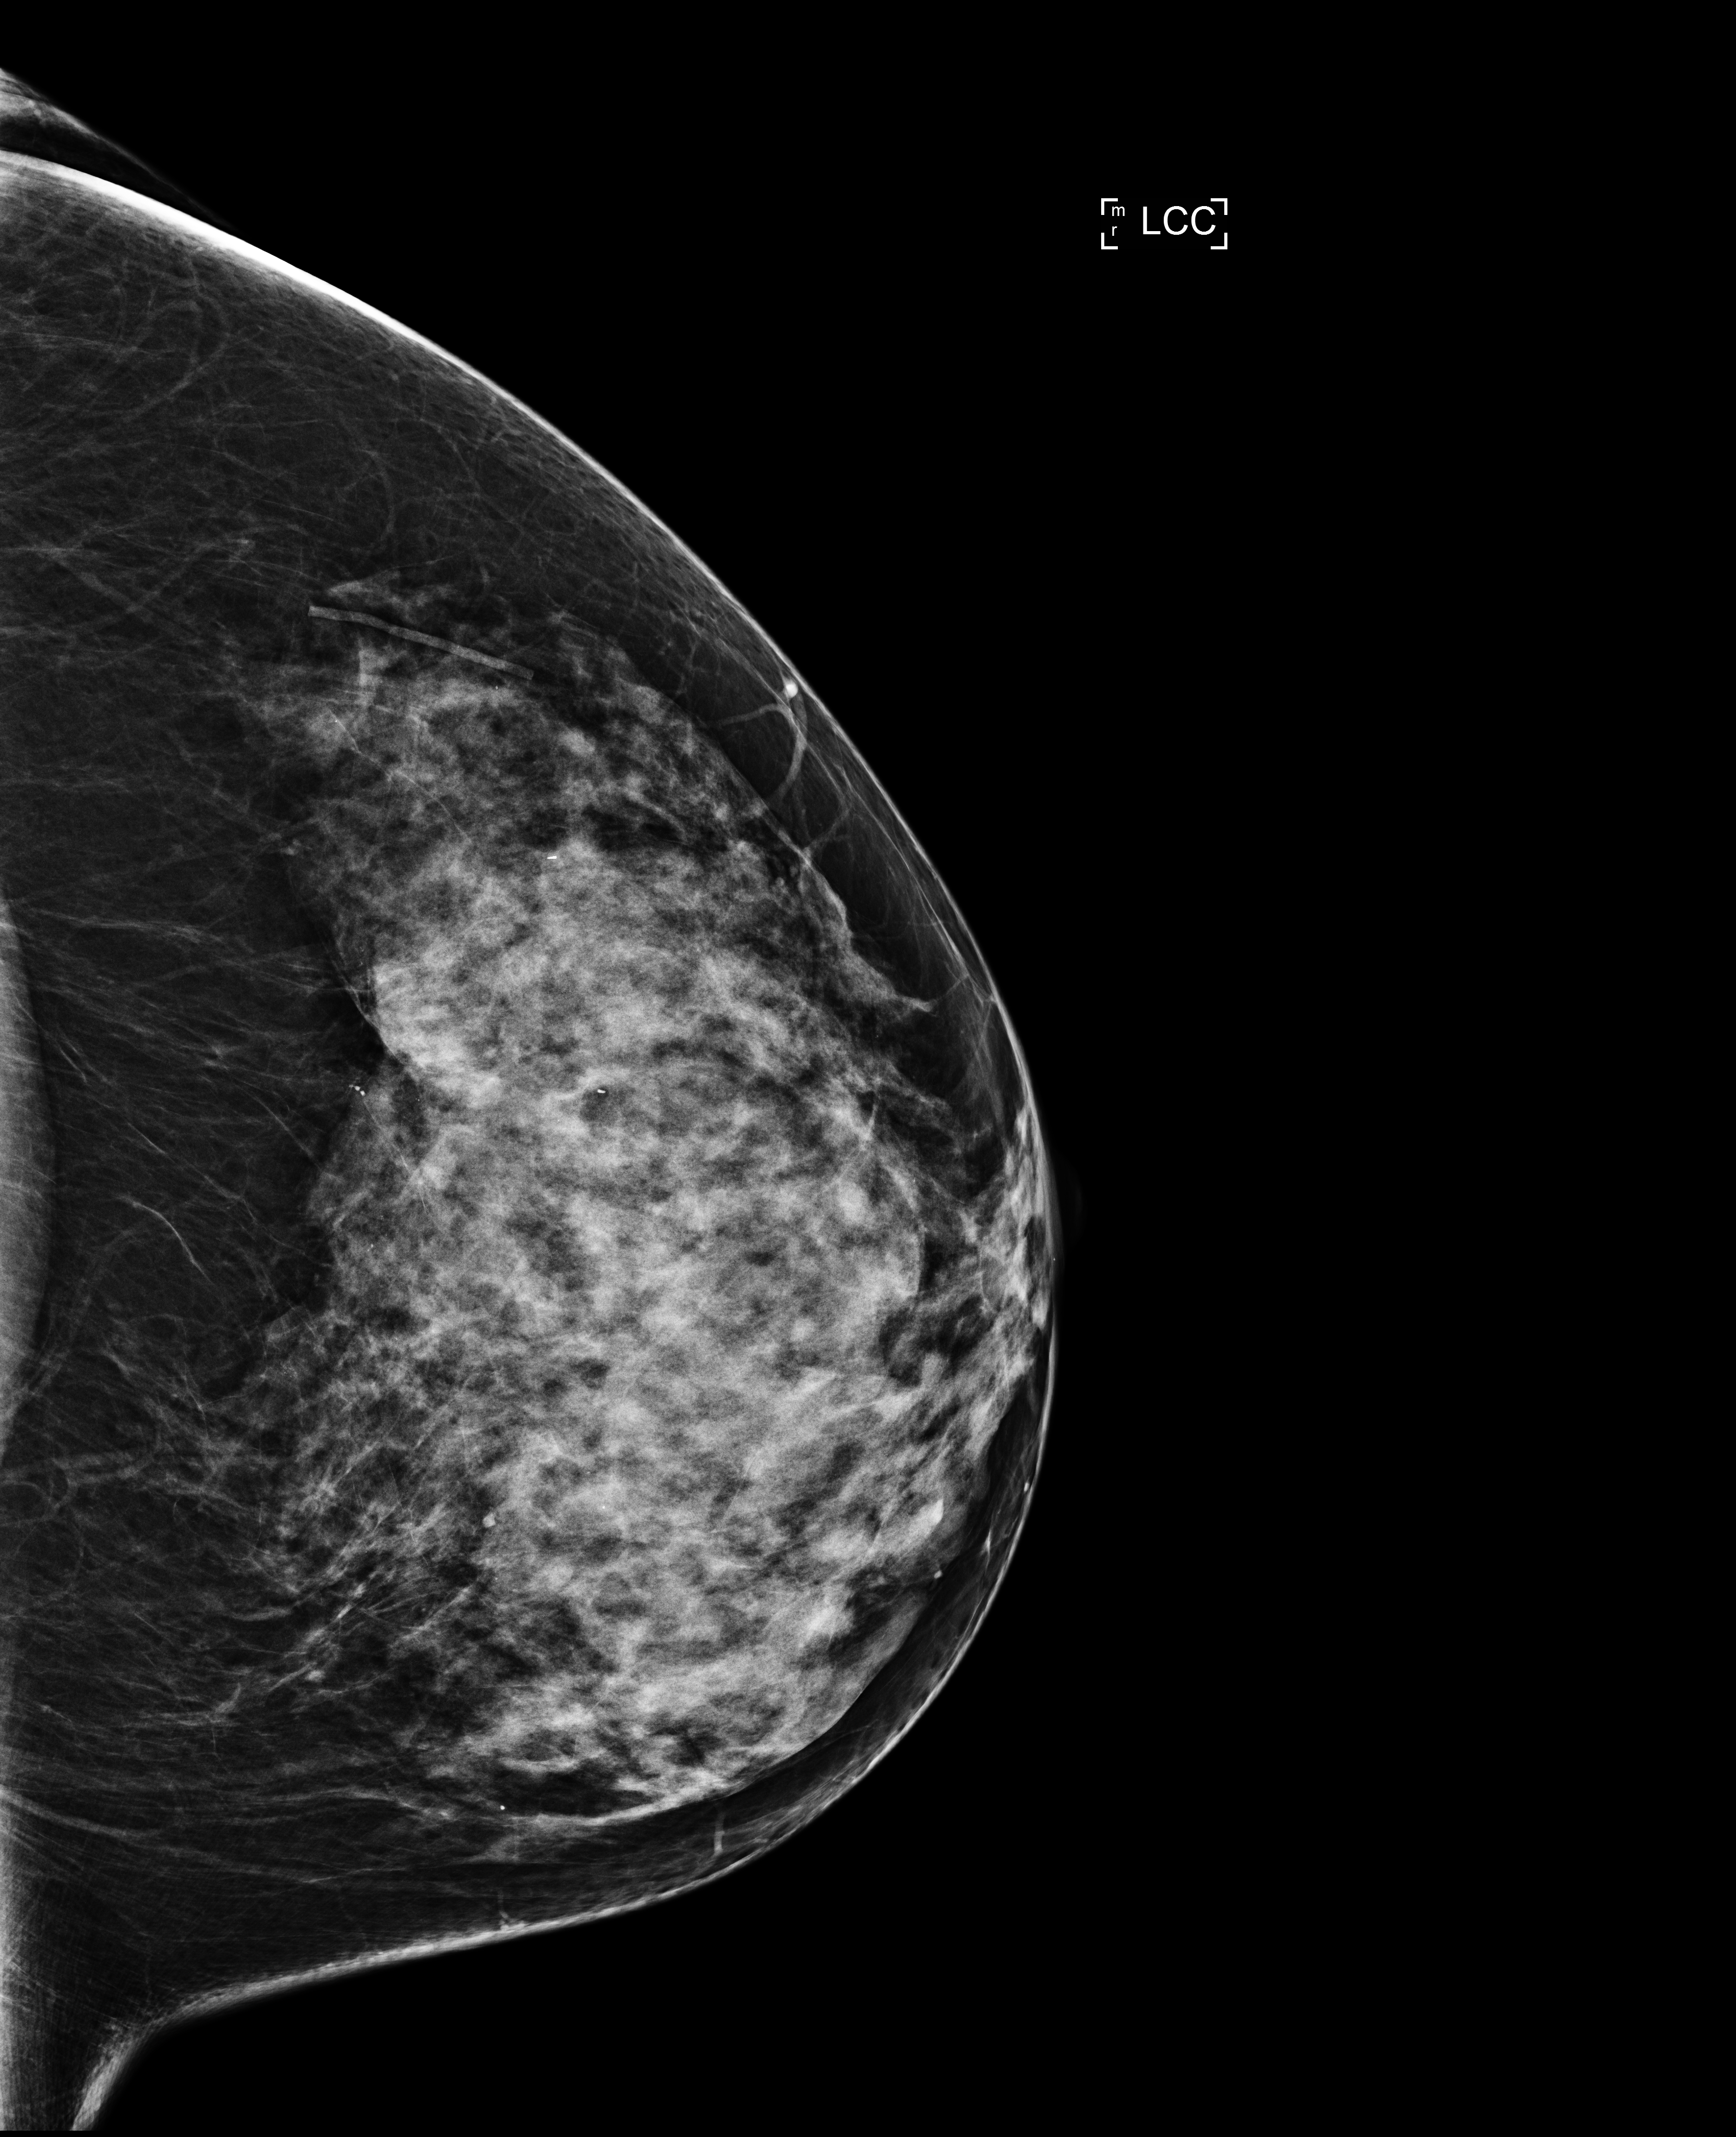
Screening examination. Female patient, age 57 years.
Image type: full-field digital mammogram. Breast: left. Projection: cranio-caudal projection.